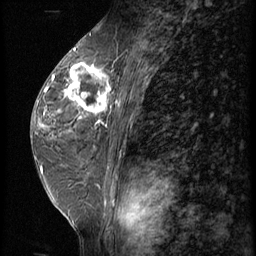
Breast MRI (dynamic contrast-enhanced), one sagittal slice. 3 images stored at this slice position (order not interpretable as contrast timing). 1.5 T. TE 4.2 ms, TR 9 ms. 2.5 mm slice thickness. 256 × 256 image matrix, field of view 180 × 180 mm. Patient: female, 44 years. Case-level facts recorded for this patient, not image findings: setting: breast cancer imaged before/during neoadjuvant chemotherapy; receptor status: triple-negative.
Structures marked on this image (semi-automatic segmentation, software-assisted and operator-edited):
- analysis volume of interest (the breast-tissue region the enhancement analysis was run in; not a lesion): bounding box <67,64,116,125> (left, top, right, bottom; pixels)
- tumour enhancement mask (voxels above the 140 % enhancement threshold inside the analysis volume of interest): <67,65,113,125>